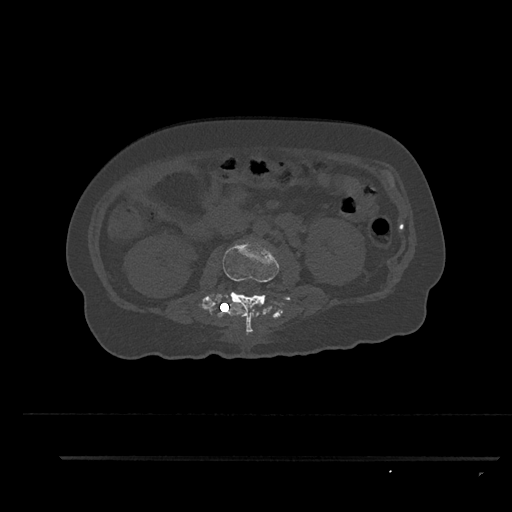
CT including the spine, one axial slice. Position 140 of 797 along the scan axis. Bone window (W 1800 / L 400 HU). 0.5 mm slice thickness. 512 × 512 image matrix. Patient: female, 44 years. From the clinical record (not read from this slice): primary cancer: renal.
Outlined on this slice (semi-automatically segmented with operator editing):
- L2 vertebra: box from (x=198, y=240) to (x=279, y=335) px